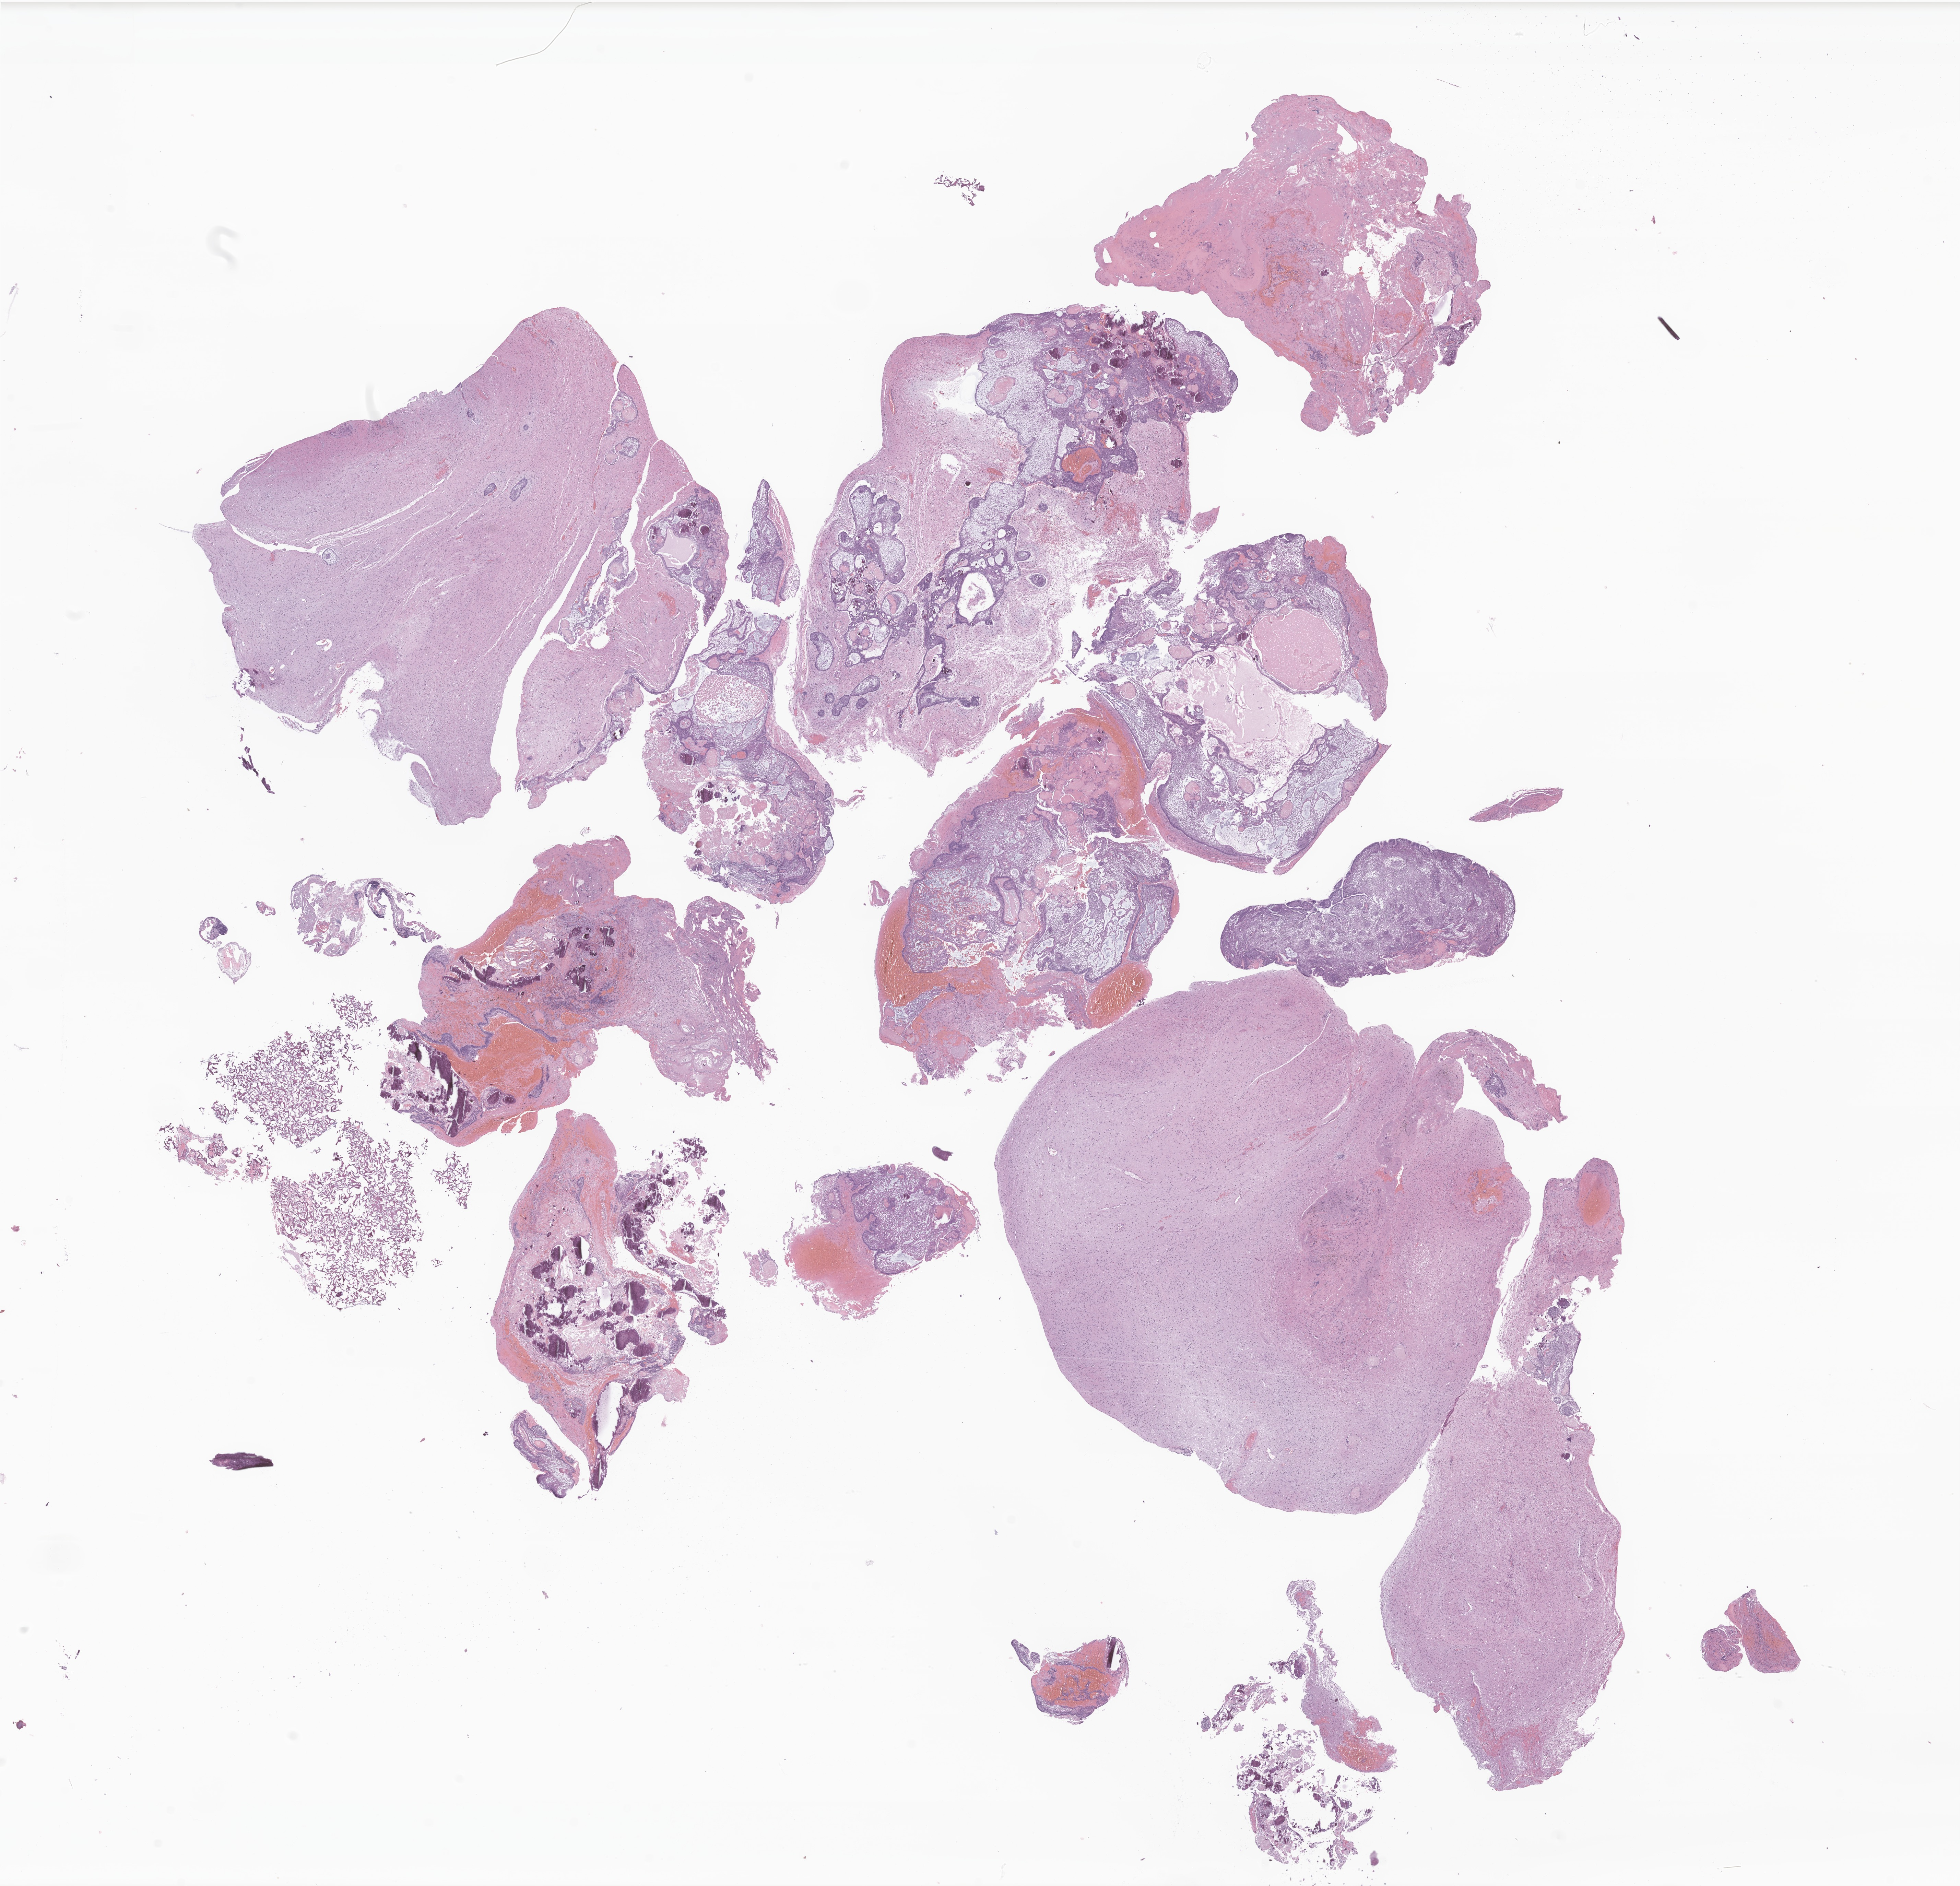
Digitized haematoxylin and eosin-stained section of tumor tissue from the brain — whole scanned area (about 24.1 x 23.2 mm) shown as a low-resolution overview, formalin-fixed paraffin-embedded section. Patient: male, age 218 months (18 years 2 months).
Diagnosis (ICD-O-3 morphology term): Craniopharyngioma, NOS.